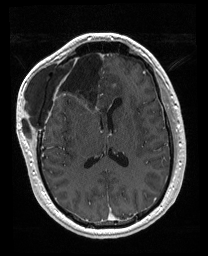
Brain MRI from a brain-tumour surgery series, one axial slice; slice 83 of 176 in the series (ordered by position); T1-weighted post-contrast; 208 × 256 image matrix, field of view 208 × 256 mm. From the clinical record (not read from this slice): histopathology: Astrocytoma; WHO grade: 4; IDH mutation: yes; tumour location: Right Orbitofrontal Anterior Temporal Insular.
Outlined on this slice (expert manual segmentation):
- previous resection cavity: bounding box [x1, y1, x2, y2] px = [56, 52, 106, 111]